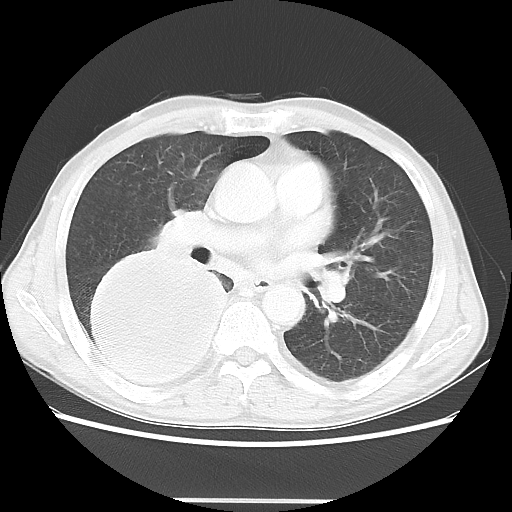
Chest CT, one axial slice. Position 25 of 48 along the scan axis. Reconstruction kernel LUNG. 100 kVp. Lung window (W 1500 / L -600 HU). 5 mm slice thickness. 512 × 512 image matrix, field of view 361 × 361 mm. Patient: male, 66 years. From the clinical record (not read from this slice): clinical TNM (as recorded): T4 N1 M1.
Annotated regions visible in this slice (rectangle marked by the reading radiologist):
- lung tumour (recorded histology: small cell carcinoma): bounding box (x1, y1, x2, y2) in pixels: (70, 242, 232, 406)